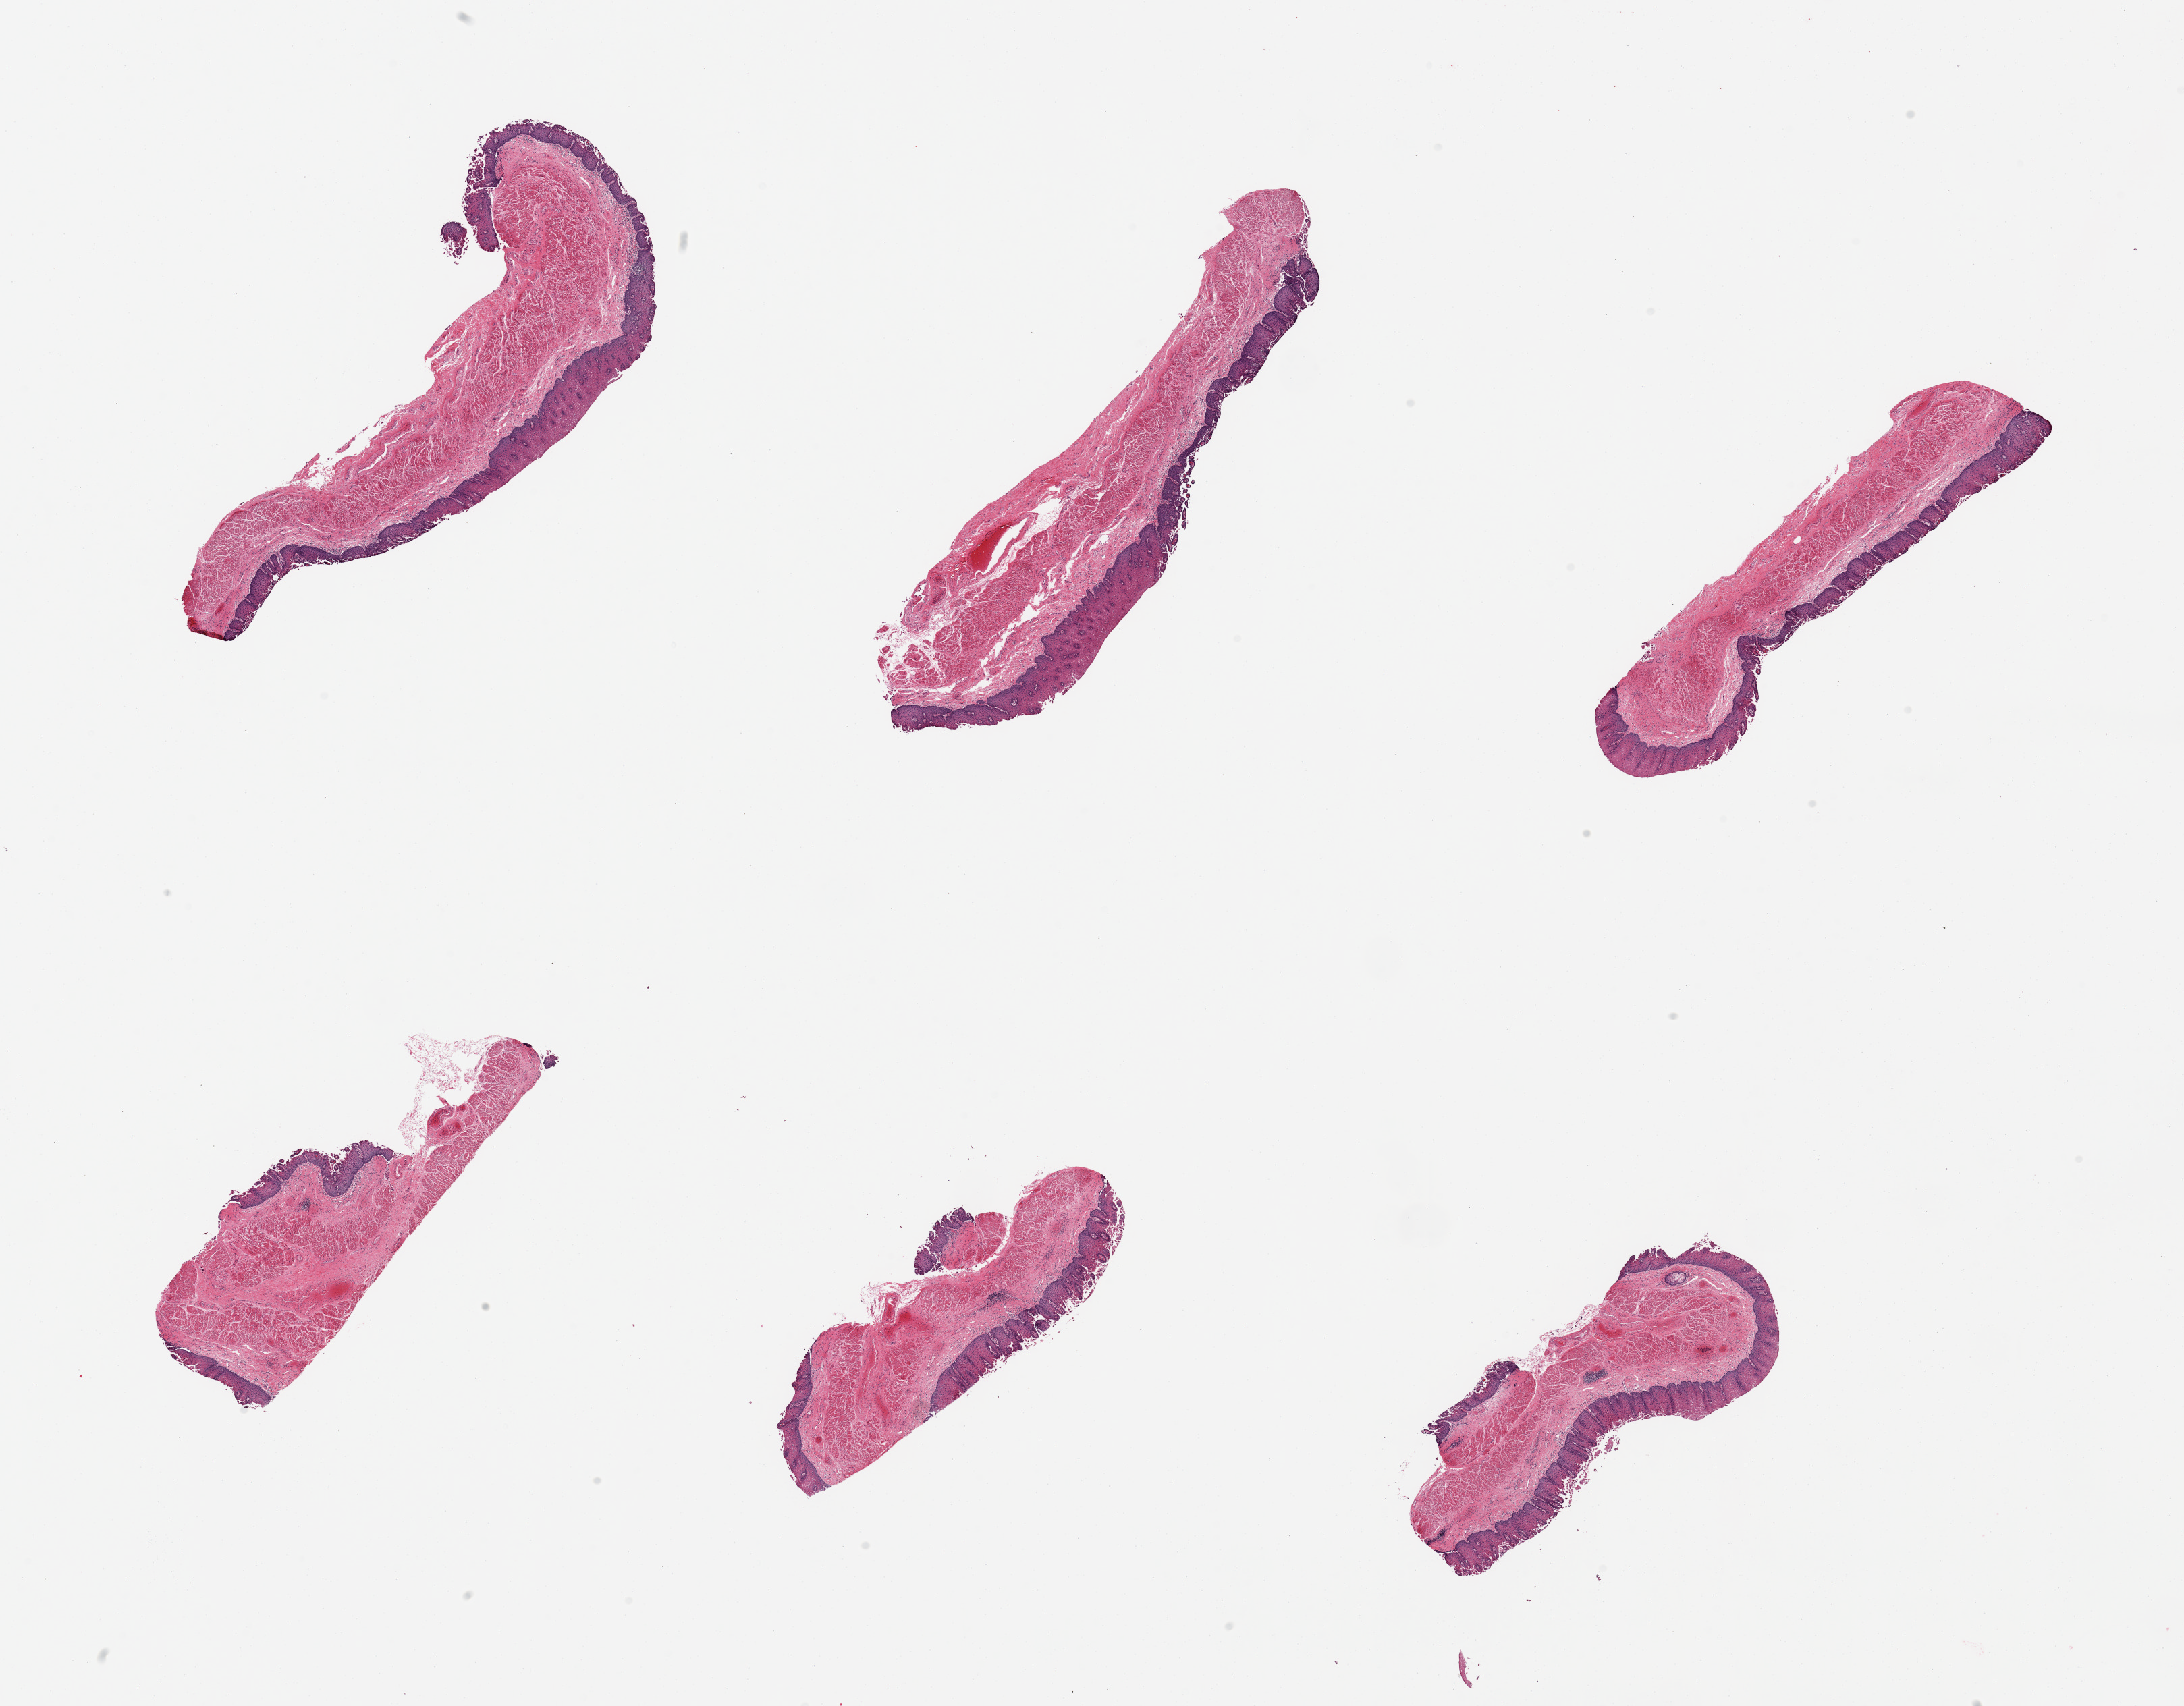
Hematoxylin and eosin (H&E) whole-slide image, brightfield, whole scanned area (about 25.6 x 20.0 mm) shown as a low-resolution overview, PAXgene-fixed, paraffin-embedded tissue, section of esophageal mucous membrane (target tissue), donor tissue sample. Donor sex: male.
Reviewer comment on this tissue sample: 6 pieces; well trimmed; squamous epithelium up to 0.5mm thick.